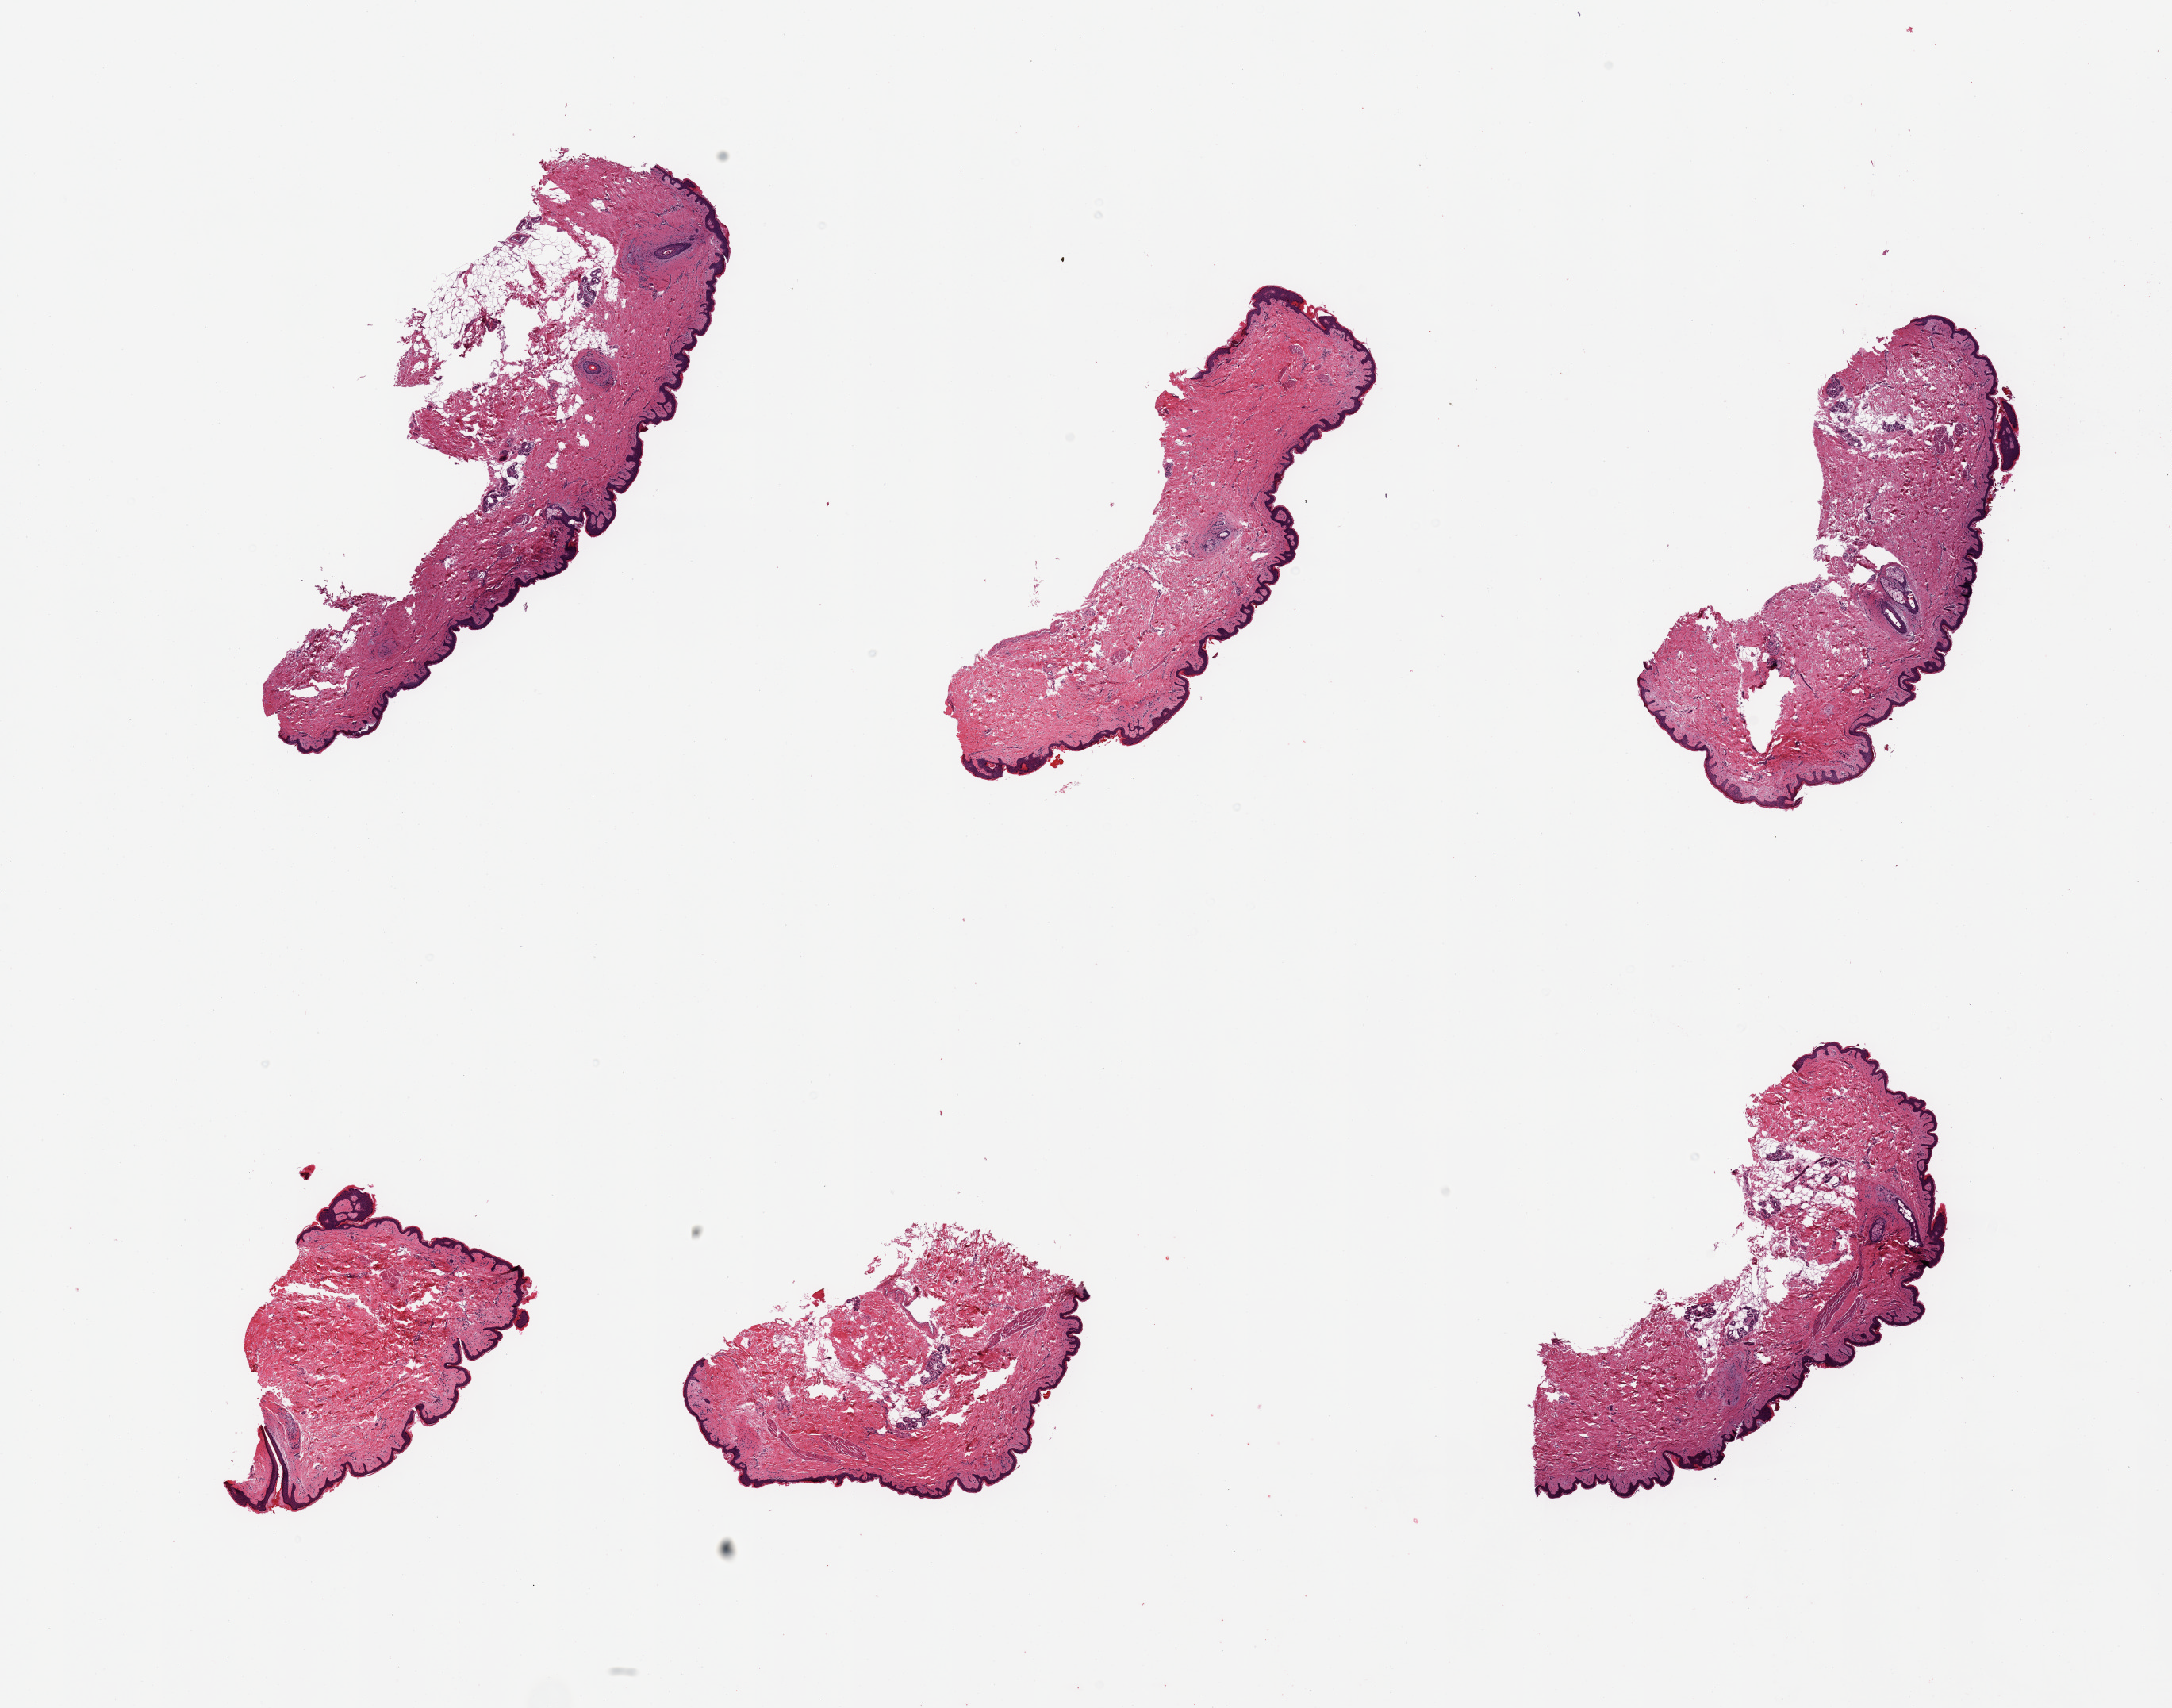
Digitized haematoxylin and eosin-stained section, shown as a low-resolution overview of the whole scanned area (about 21.7 x 17.0 mm, acquisition: 20x scan). PAXgene-fixed, paraffin-embedded tissue. Section of skin of suprapubic region (target tissue). Tissue donor sample.
Reviewer comment on this tissue sample: 6 pieces; up too 30% dermal fat.